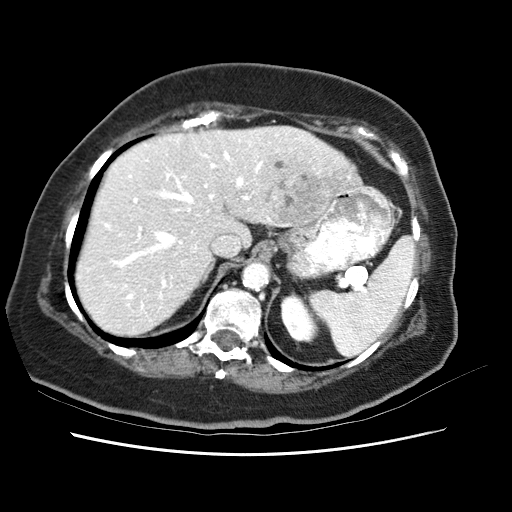
Contrast-enhanced abdominal CT (liver protocol), one axial slice; slice 45 of 62 in the series (ordered by position); 120 kVp; soft-tissue window (W 400 / L 40 HU); 2.5 mm slice thickness; 512 × 512 image matrix, field of view 340 × 340 mm. Case-level facts recorded for this patient, not image findings: diagnosis: hepatocellular carcinoma (patient treated with transarterial chemoembolisation; whether this scan precedes or follows treatment is not stated here); TNM stage (as recorded): Stage-I; Child-Pugh class: B.
Structures marked on this image (semi-automatically segmented with operator editing):
- liver parenchyma outside the tumour (the mass and vessels are separate outlines, so this box may not span the whole liver): bounding box (x1, y1, x2, y2) in pixels: (82, 125, 344, 328)
- mass: (257, 144, 333, 223)
- liver vessels: (114, 132, 306, 311)